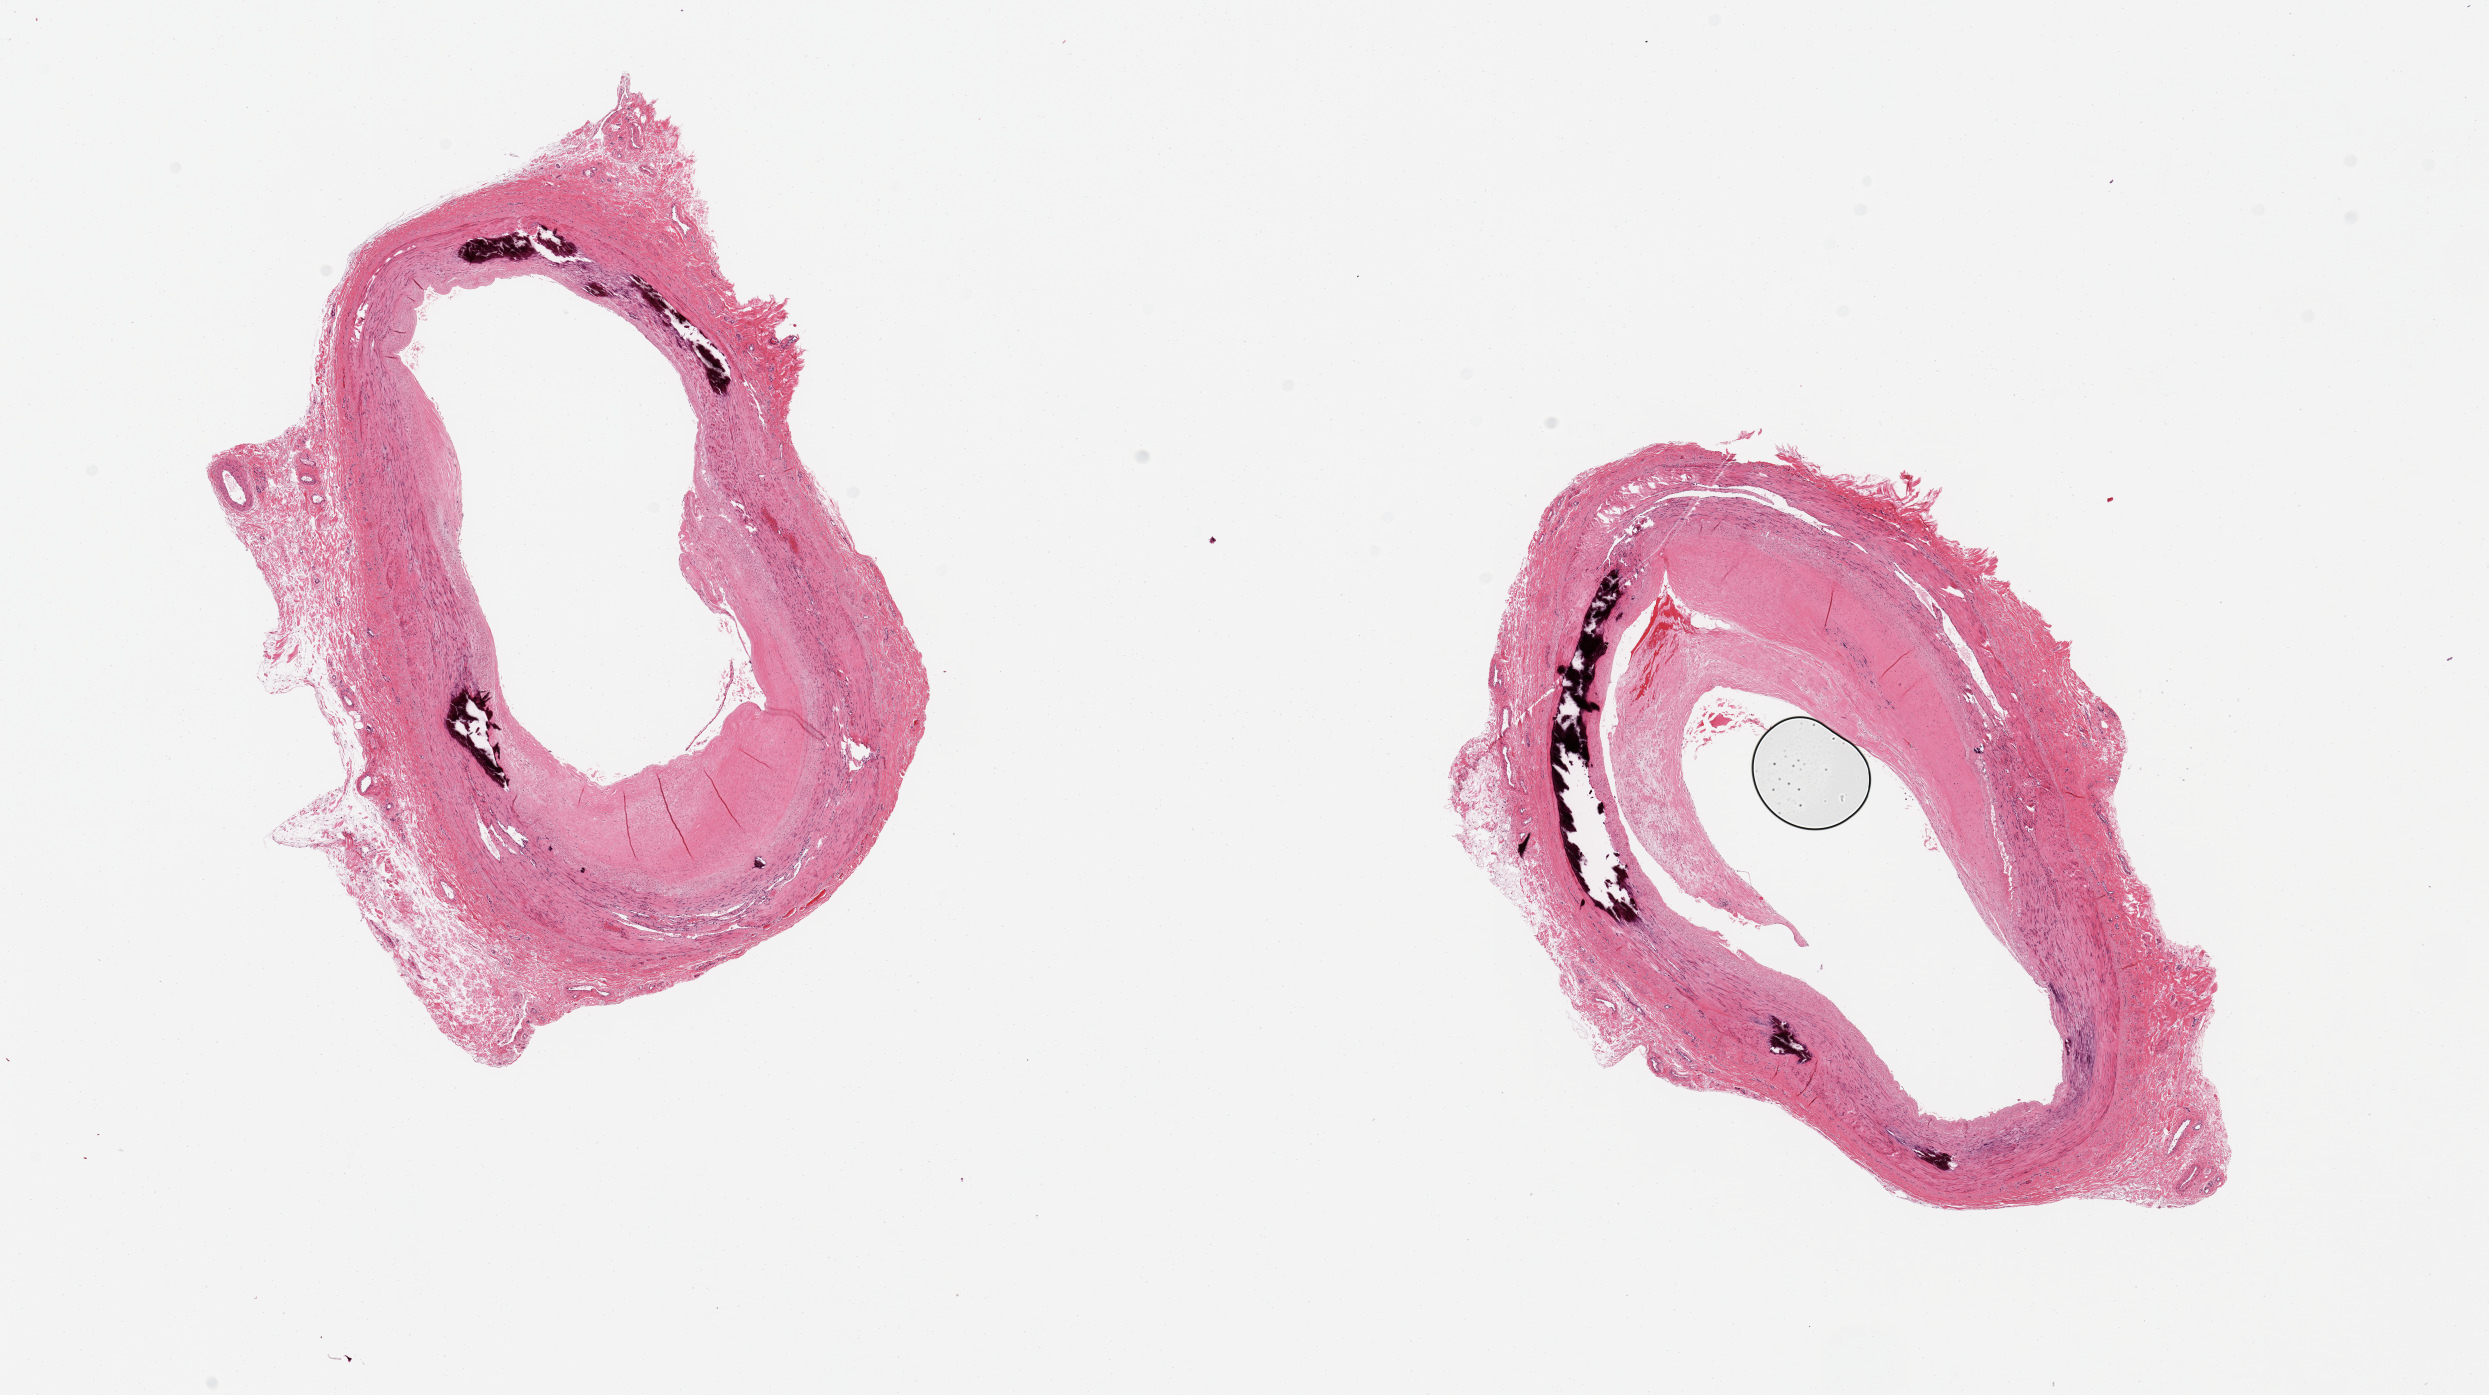
Haematoxylin and eosin whole-slide image — shown as a low-resolution overview of the whole scanned area (about 19.7 x 11.0 mm, from a 20x scan), PAXgene-fixed, paraffin-embedded tissue, target tissue: tibial artery, donor tissue sample. Male donor.
Review note (as recorded): 2 pieces, prominent Monckeberg medial sclerosis; ~40% occlusve atherosis.